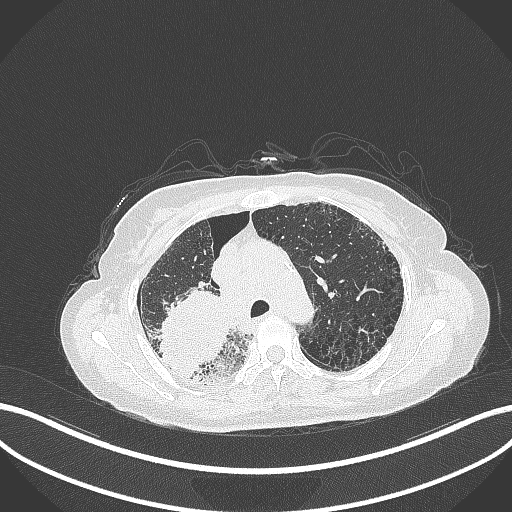
Chest CT, one axial slice; slice 250 of 408 in the series (ordered by position); reconstruction kernel B70f; 120 kVp; lung window (W 1500 / L -600 HU); 1 mm slice thickness; 512 × 512 image matrix. Female patient, age 64 years. From the clinical record (not read from this slice): clinical TNM (as recorded): T3 N3 M0.
Structures marked on this image (bounding box drawn by a radiologist):
- lung tumour (recorded histology: squamous cell carcinoma): bounding box (x1, y1, x2, y2) in pixels: (158, 293, 233, 382)